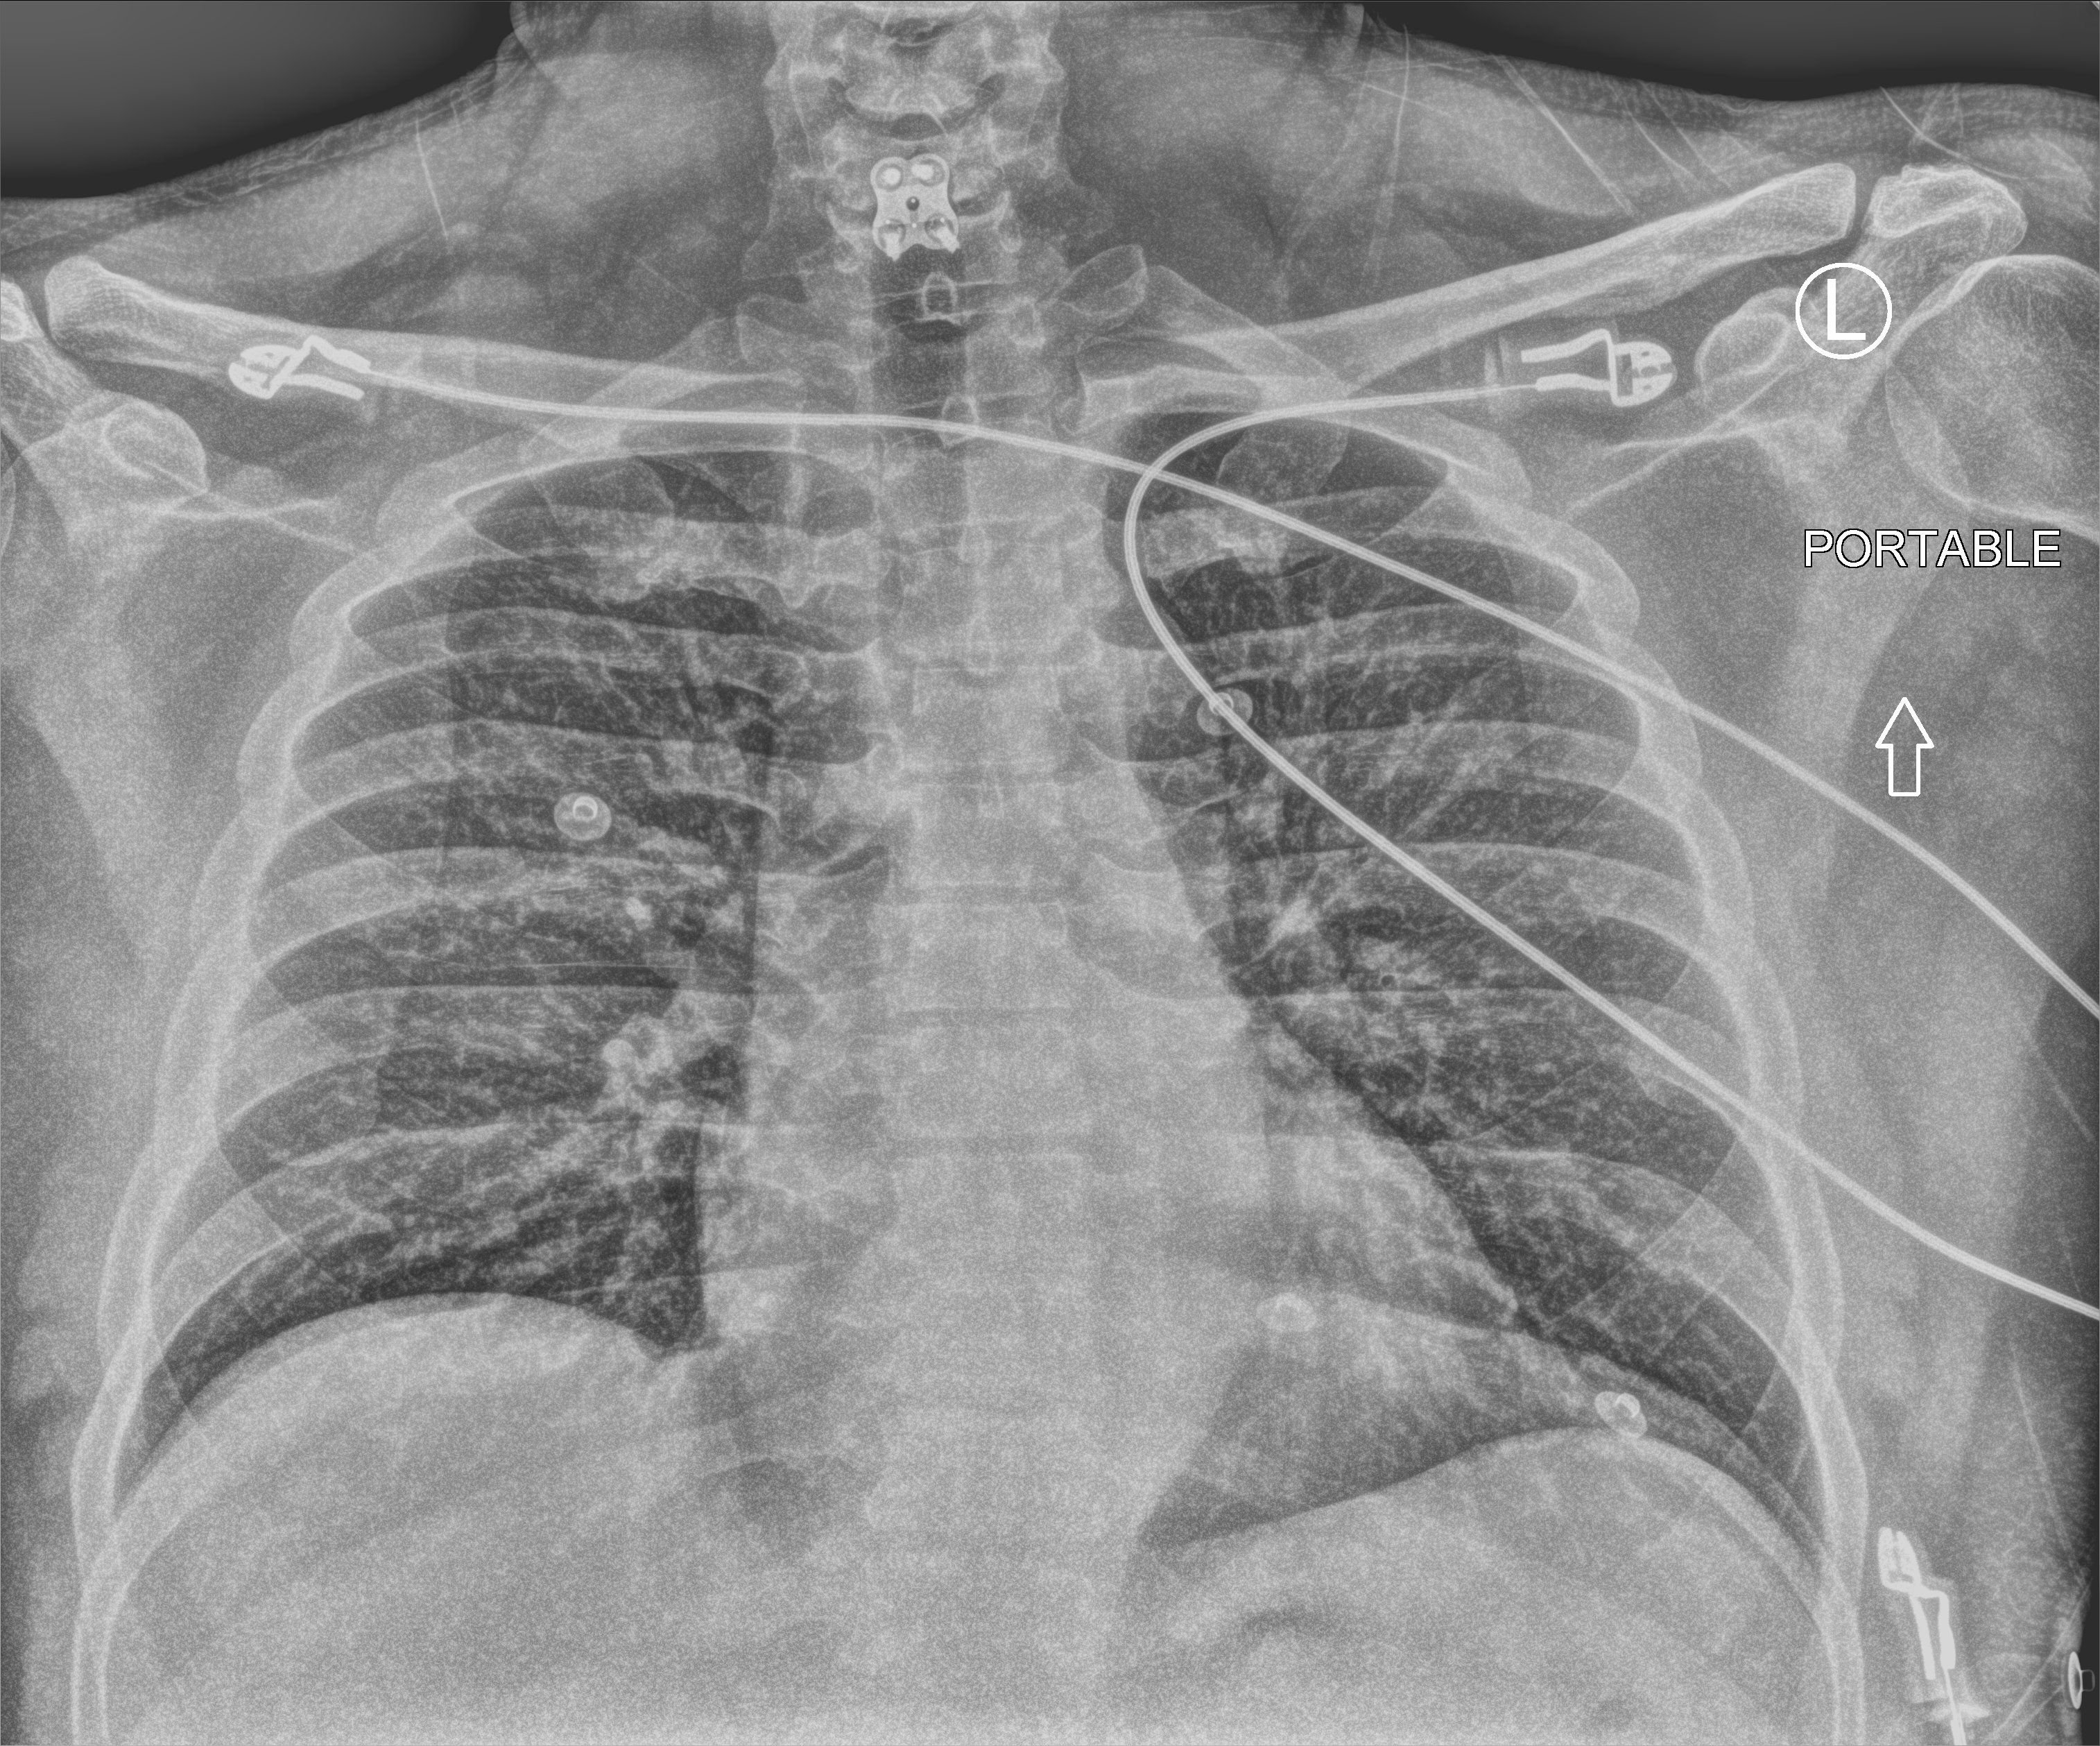
Chest X-ray (portable); anteroposterior (AP) projection. Male patient hospitalised with COVID-19, age 18–59 years.
From the hospital-stay record, not from the radiograph (when in the stay this image was taken is not recorded): other chronic lung disease (admission record): no; mechanically ventilated during this hospital stay: no.